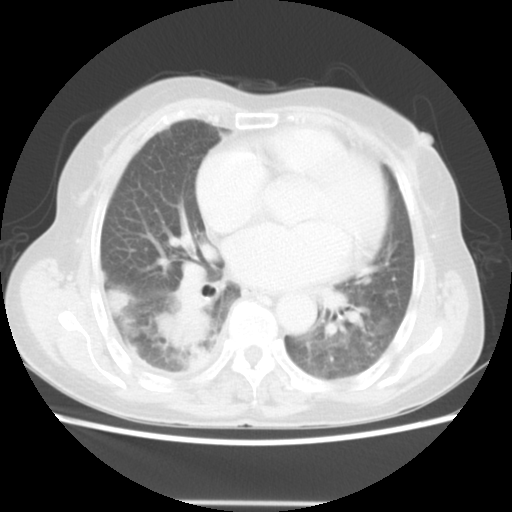
Chest CT, one axial slice; slice 24 of 52 in the series (ordered by position); lung window (W 1500 / L -600 HU); 5 mm slice thickness; 512 × 512 image matrix. Patient: female, 67 years. From the clinical record (not read from this slice): clinical TNM (as recorded): T3 N1 M1.
Outlined on this slice (bounding box drawn by a radiologist):
- lung tumour (recorded histology: adenocarcinoma): bounding box [x1, y1, x2, y2] px = [156, 289, 215, 373]